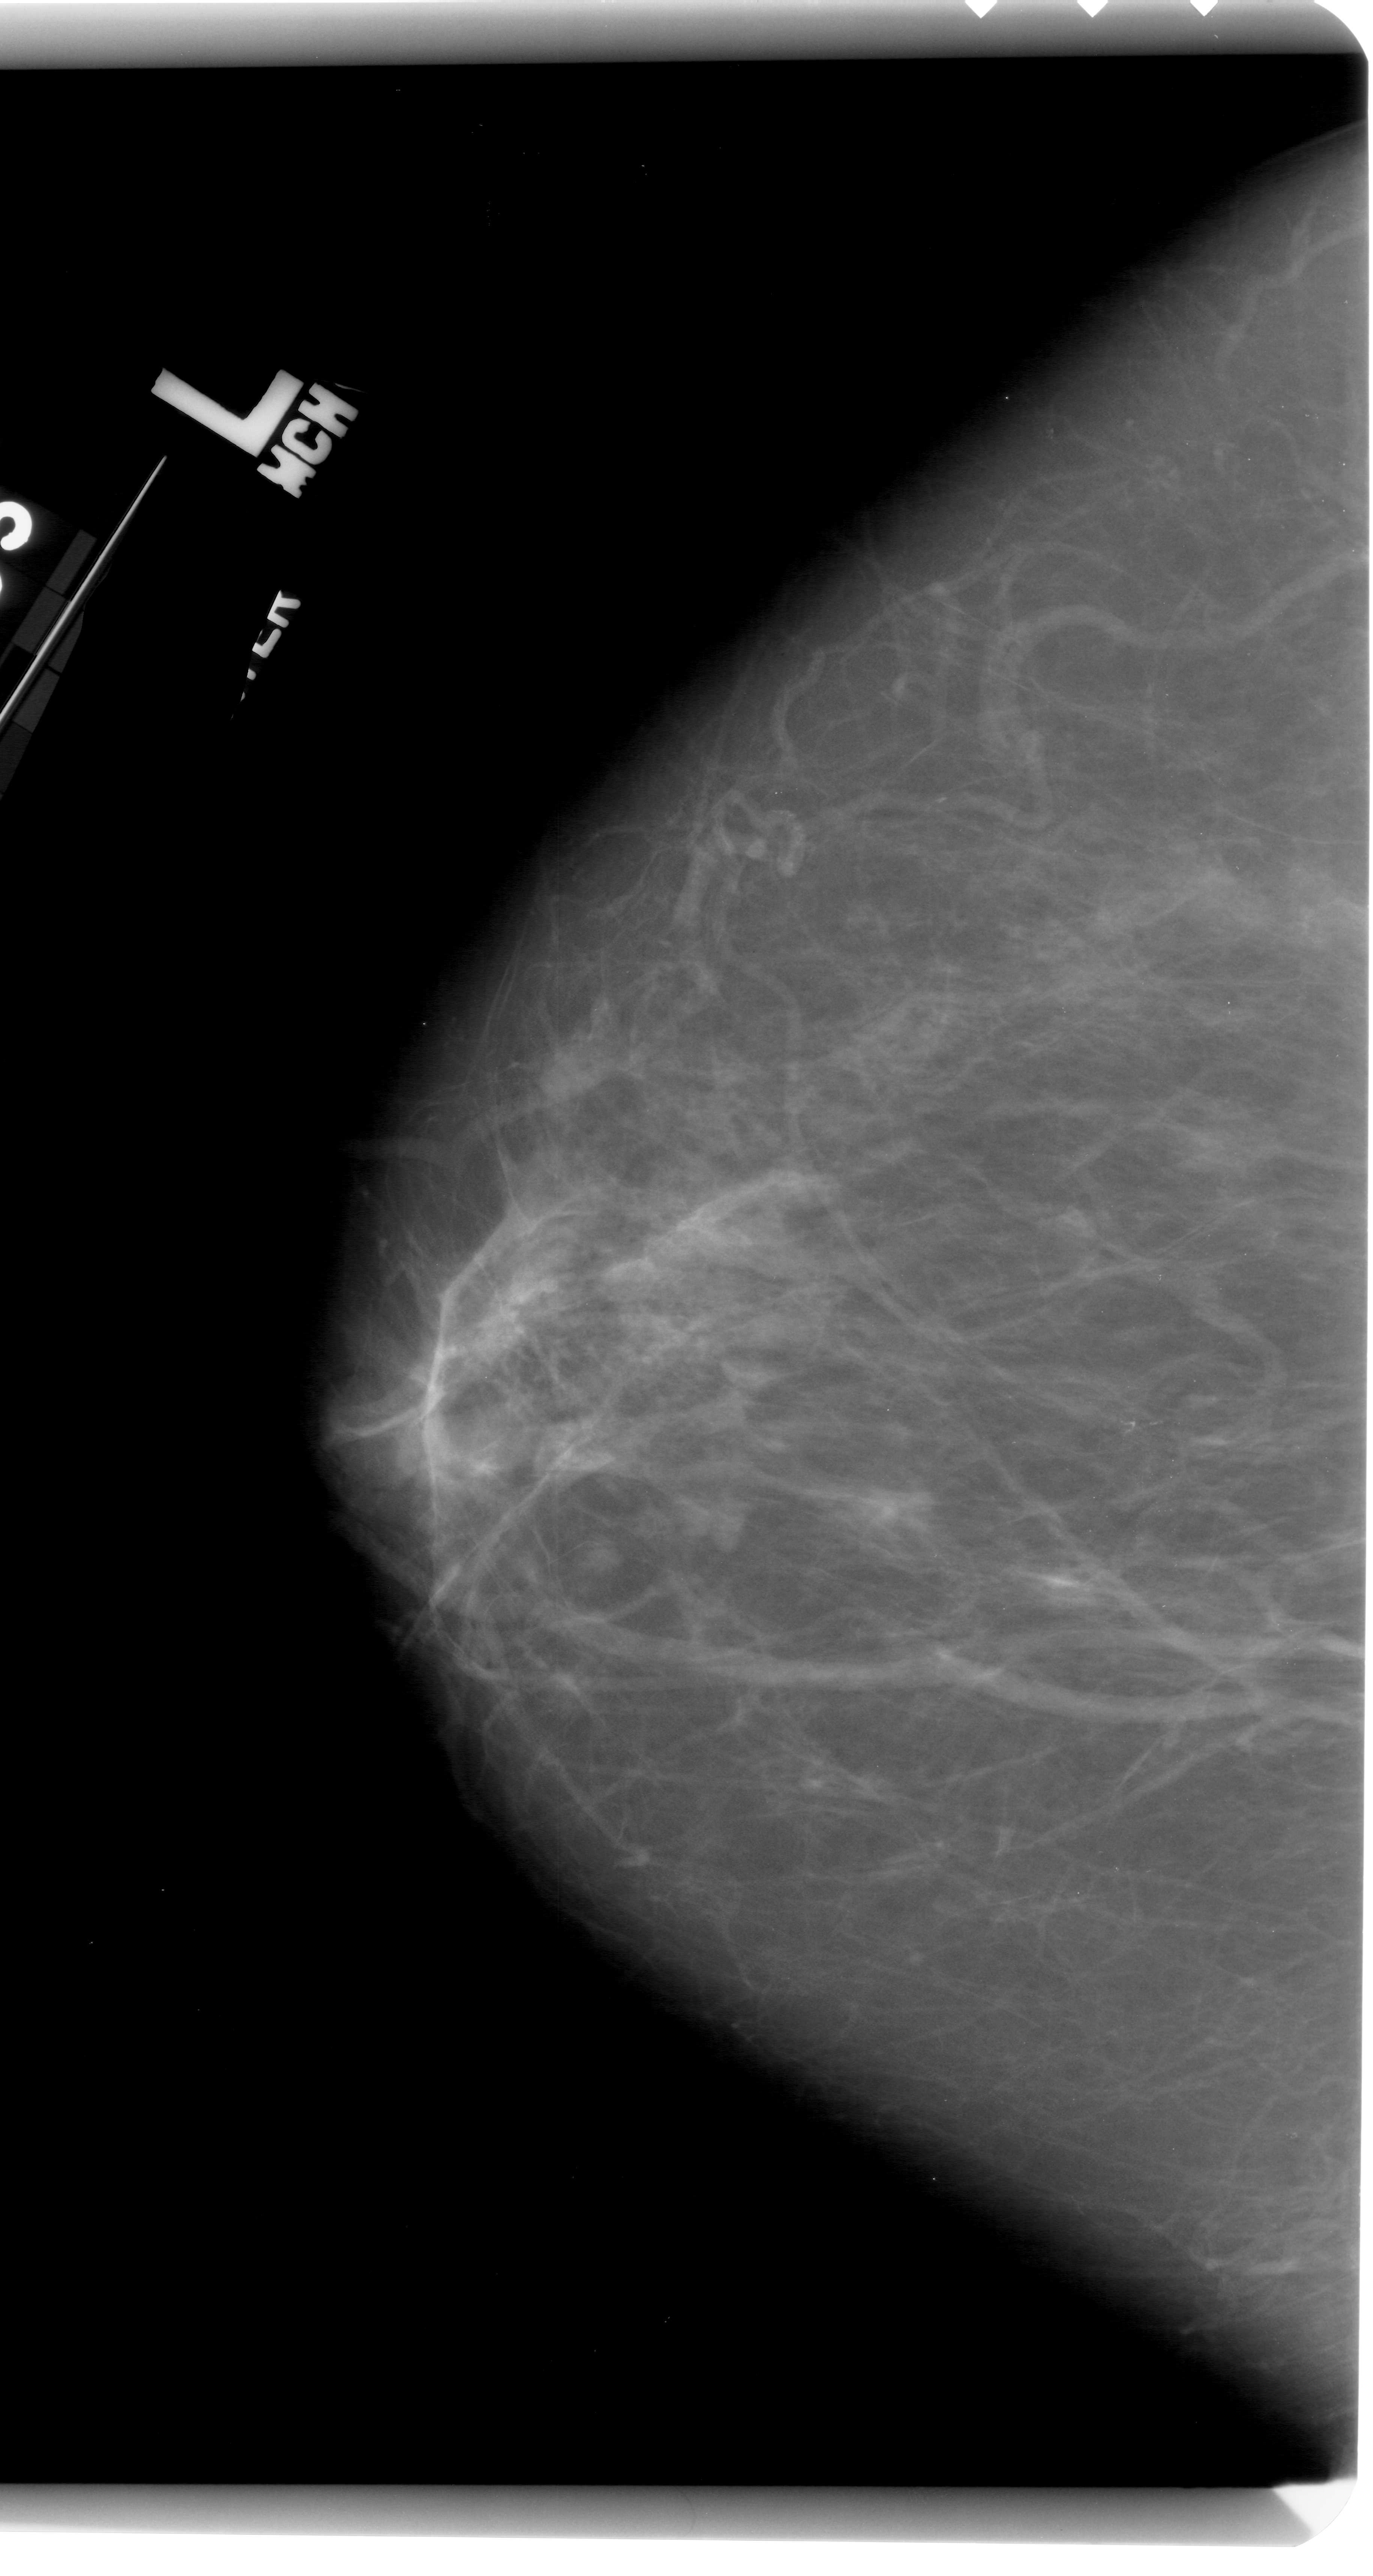
Digitized screen-film mammogram, left breast, craniocaudal (CC) view, breast composition: scattered fibroglandular densities (BI-RADS density category 2 of 4).
- Marked findings (only marked abnormalities are described; nothing is implied about the rest of the image): calcifications, morphology fine linear branching, distribution linear; BI-RADS assessment category 4; subtlety rating 2 on a 1 (subtle) to 5 (obvious) scale; pathology (as recorded): malignant.